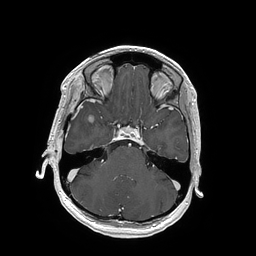
Brain MRI from a brain-tumour surgery series, one axial slice. Slice 119 of 202 in the series (ordered by position). T1-weighted post-contrast. 1 mm slice thickness. 256 × 256 image matrix. From the clinical record (not read from this slice): histopathology: Glioblastoma; WHO grade: 4; IDH mutation: no; tumour location: Right Insular.
Annotated regions visible in this slice (outlined manually by an expert reader):
- tumour: bounding box <87,116,94,123> (left, top, right, bottom; pixels)